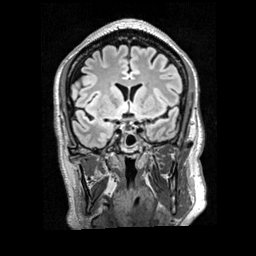
Brain MRI from a brain-tumour surgery series, one coronal slice. Position 123 of 200 along the scan axis. T2 FLAIR. 1 mm slice thickness. 256 × 256 image matrix. Case-level facts recorded for this patient, not image findings: histopathology: Glioblastoma; WHO grade: 4; IDH mutation: no; tumour location: Right Frontal.
Structures marked on this image (manually delineated by an expert):
- tumour: bounding box <87,74,94,80> (left, top, right, bottom; pixels)